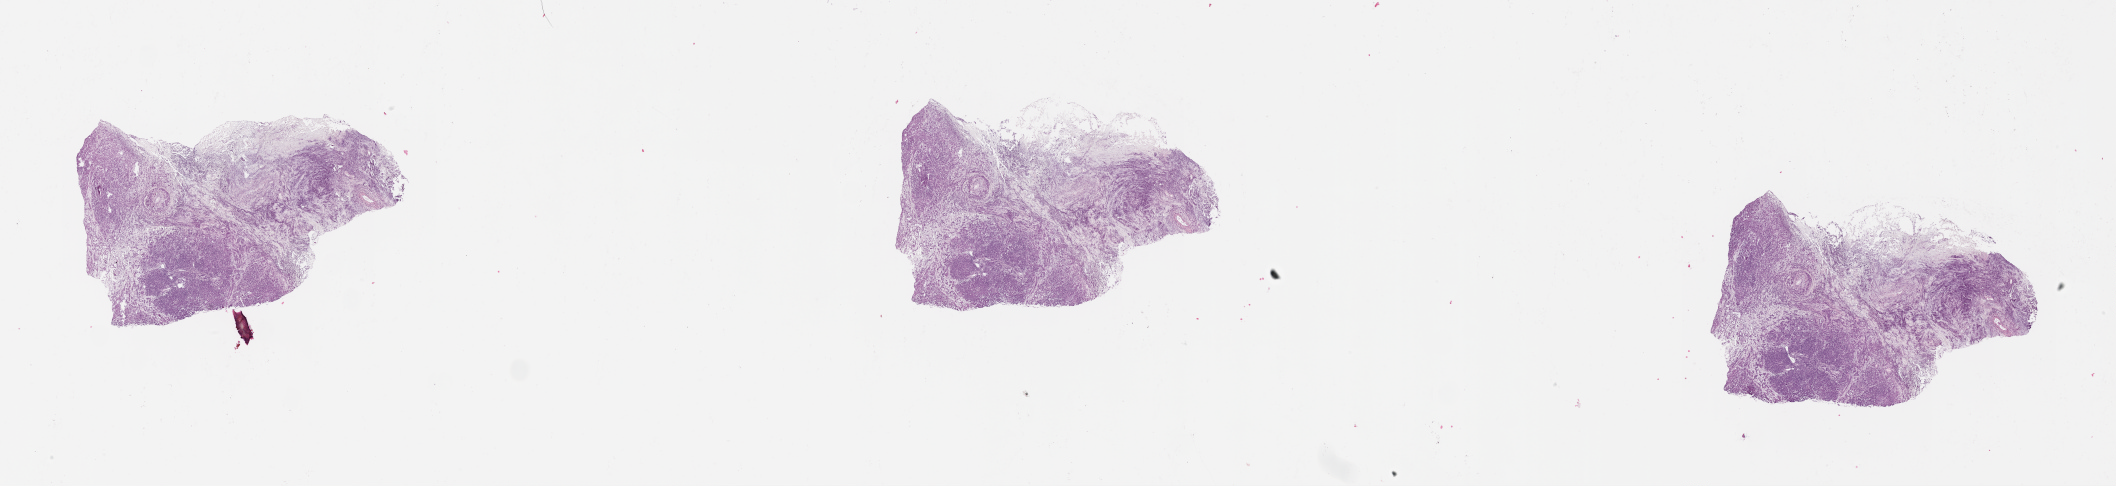
Digitized H&E tissue section (whole slide) — shown as a low-resolution overview of the whole scanned area (about 34.1 x 7.8 mm); tumour tissue sample, sampled site: pancreas. 66-year-old female patient. Histologic grade: G3 (poorly differentiated). Slide review estimates, as recorded: tumour nuclei 30%, necrosis 2%.
Primary tumour site (as recorded): head. Diagnosis: Infiltrating duct carcinoma, NOS. AJCC pathologic stage: III.